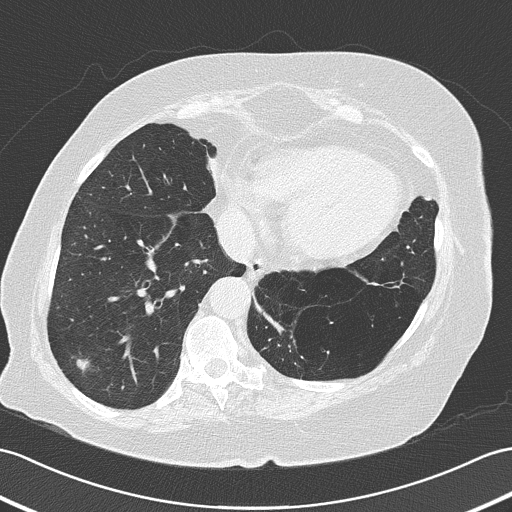
Chest CT (low-dose screening protocol), one axial image. Baseline annual screen. Lung window (W 1500 / L -600 HU). 2 mm slice thickness. 120 kVp. 512 × 512 image matrix, field of view 353 × 353 mm. Female, age 73 years at enrolment.
Lesion marked by an expert reader, bounding box [x1, y1, x2, y2] px = [52, 335, 102, 383]. The screening reader recorded 4 non-calcified nodules or masses ≥4 mm on this exam (right lower lobe, right upper lobe, left upper lobe, left lower lobe); which of them this box marks is not recorded. Lung cancer was diagnosed 50 days after this screen: adenocarcinoma, NOS, right lower lobe, poorly differentiated (G3), stage IB (AJCC 6th edition), 17 mm at pathology.